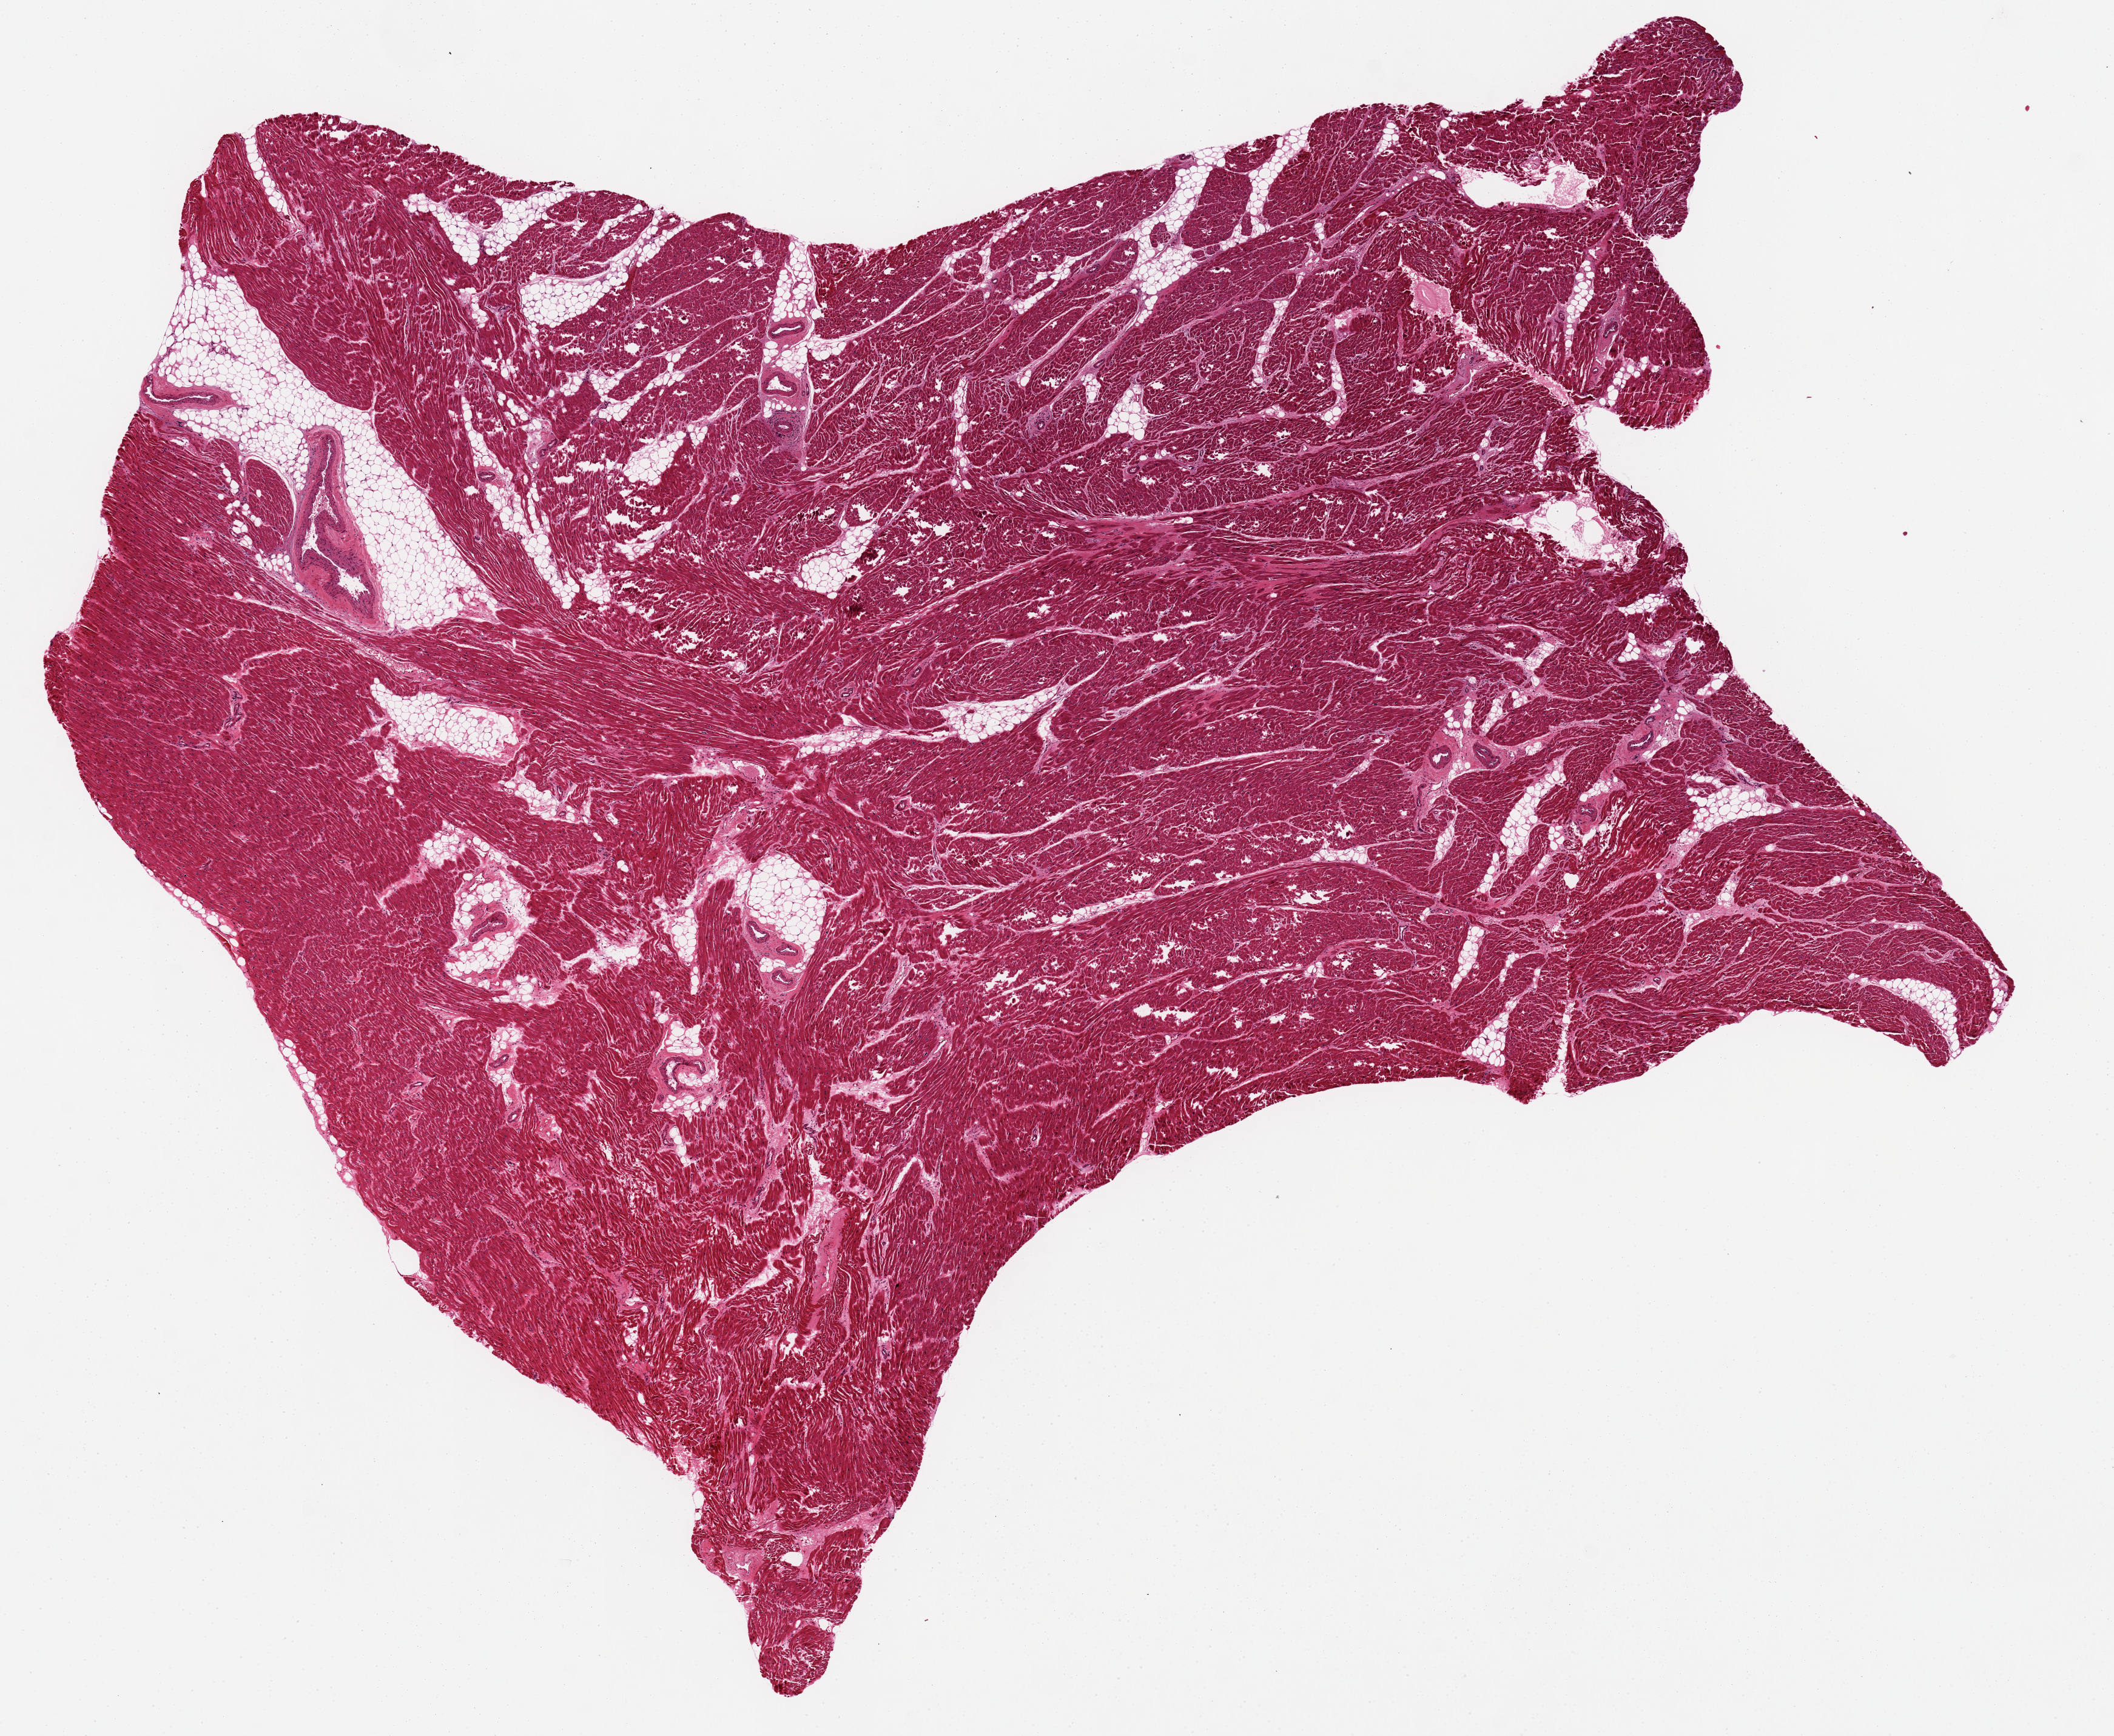
Digitized H&E-stained section, a low-resolution overview of the entire scanned area, about 13.8 x 11.3 mm. PAXgene-fixed paraffin-embedded (PFPE) section. Section of heart (target tissue). Donor tissue sample. Donor sex: male.
Reviewer comment on this tissue sample: Minimal ischemic changes.